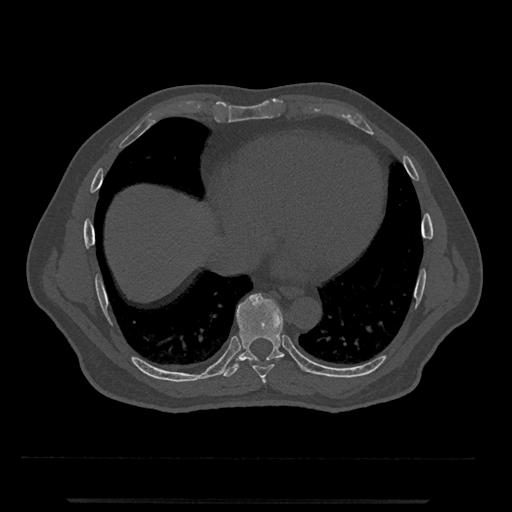
CT including the spine, one axial slice; position 597 of 797 along the scan axis; reconstruction kernel Br40s/3; 120 kVp; bone window (W 1800 / L 400 HU); 512 × 512 image matrix, field of view 419 × 419 mm. Patient: male, 63 years. Case-level facts recorded for this patient, not image findings: primary cancer: prostate.
Outlined on this slice (semi-automatically segmented with operator editing):
- T7 vertebra: bounding box <262,376,266,383> (left, top, right, bottom; pixels)
- T8 vertebra: <252,364,274,378>
- T9 vertebra: <221,293,303,377>